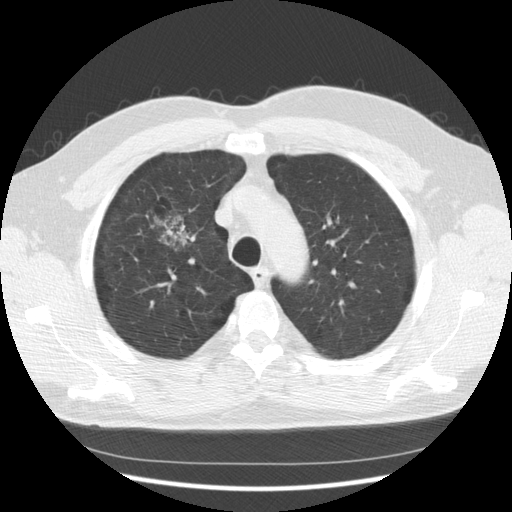
Low-dose screening chest CT, one axial slice; position 96 of 133 along the scan axis; 140 kVp; lung window (W 1500 / L -600 HU); 2.5 mm slice thickness; 512 × 512 image matrix, field of view 369 × 369 mm.
Outlined on this slice (expert manual segmentation):
- lesion 1 (tumor, upper lobe of right lung): bounding box (x1, y1, x2, y2) in pixels: (159, 216, 189, 246)